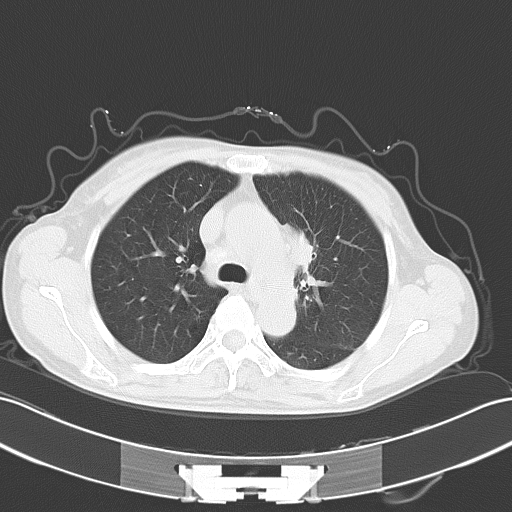
Chest CT, one axial slice. Position 39 of 54 along the scan axis. Lung window (W 1500 / L -600 HU). 5 mm slice thickness. 512 × 512 image matrix, field of view 353 × 353 mm. Patient: female, 50 years. Case-level facts recorded for this patient, not image findings: clinical TNM (as recorded): T2a N1 M1c.
Annotated regions visible in this slice (rectangle marked by the reading radiologist):
- lung tumour (recorded histology: adenocarcinoma): bounding box [x1, y1, x2, y2] px = [290, 215, 316, 274]